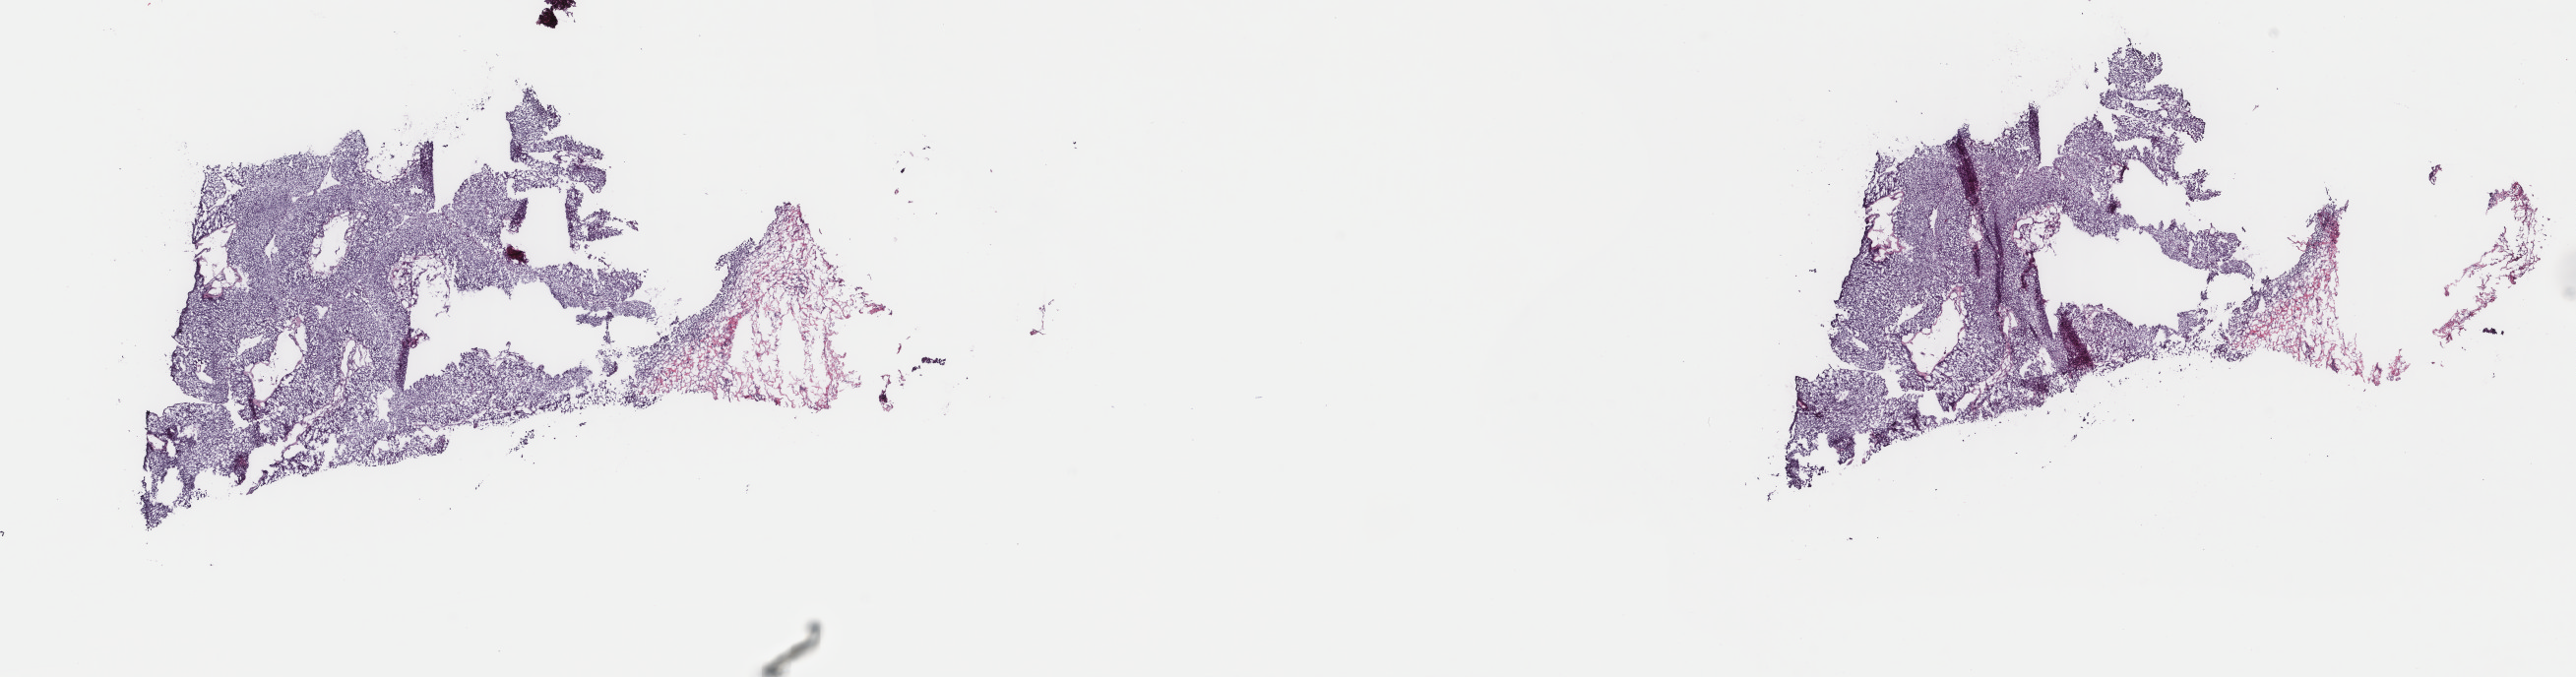
Digitized Hematoxylin and eosin (H&E) stained tissue section (whole slide) — whole scanned area (about 20.8 x 5.5 mm) shown as a low-resolution overview. Frozen section from the top of the tissue portion. Primary tumour sample from the bladder. Male, age 75 years at initial diagnosis. Histologic grade: low grade. Pathologist review of this section (percent, as recorded): tumour cells 85%, tumour nuclei 85%, normal cells 0%, stromal cells 15%, necrosis 0%. Inflammatory infiltration, as recorded: lymphocyte infiltration 2%, monocyte infiltration 1%, neutrophil infiltration 1%.
Pathologic diagnosis: Papillary transitional cell carcinoma. AJCC pathologic stage: II (7th edition).